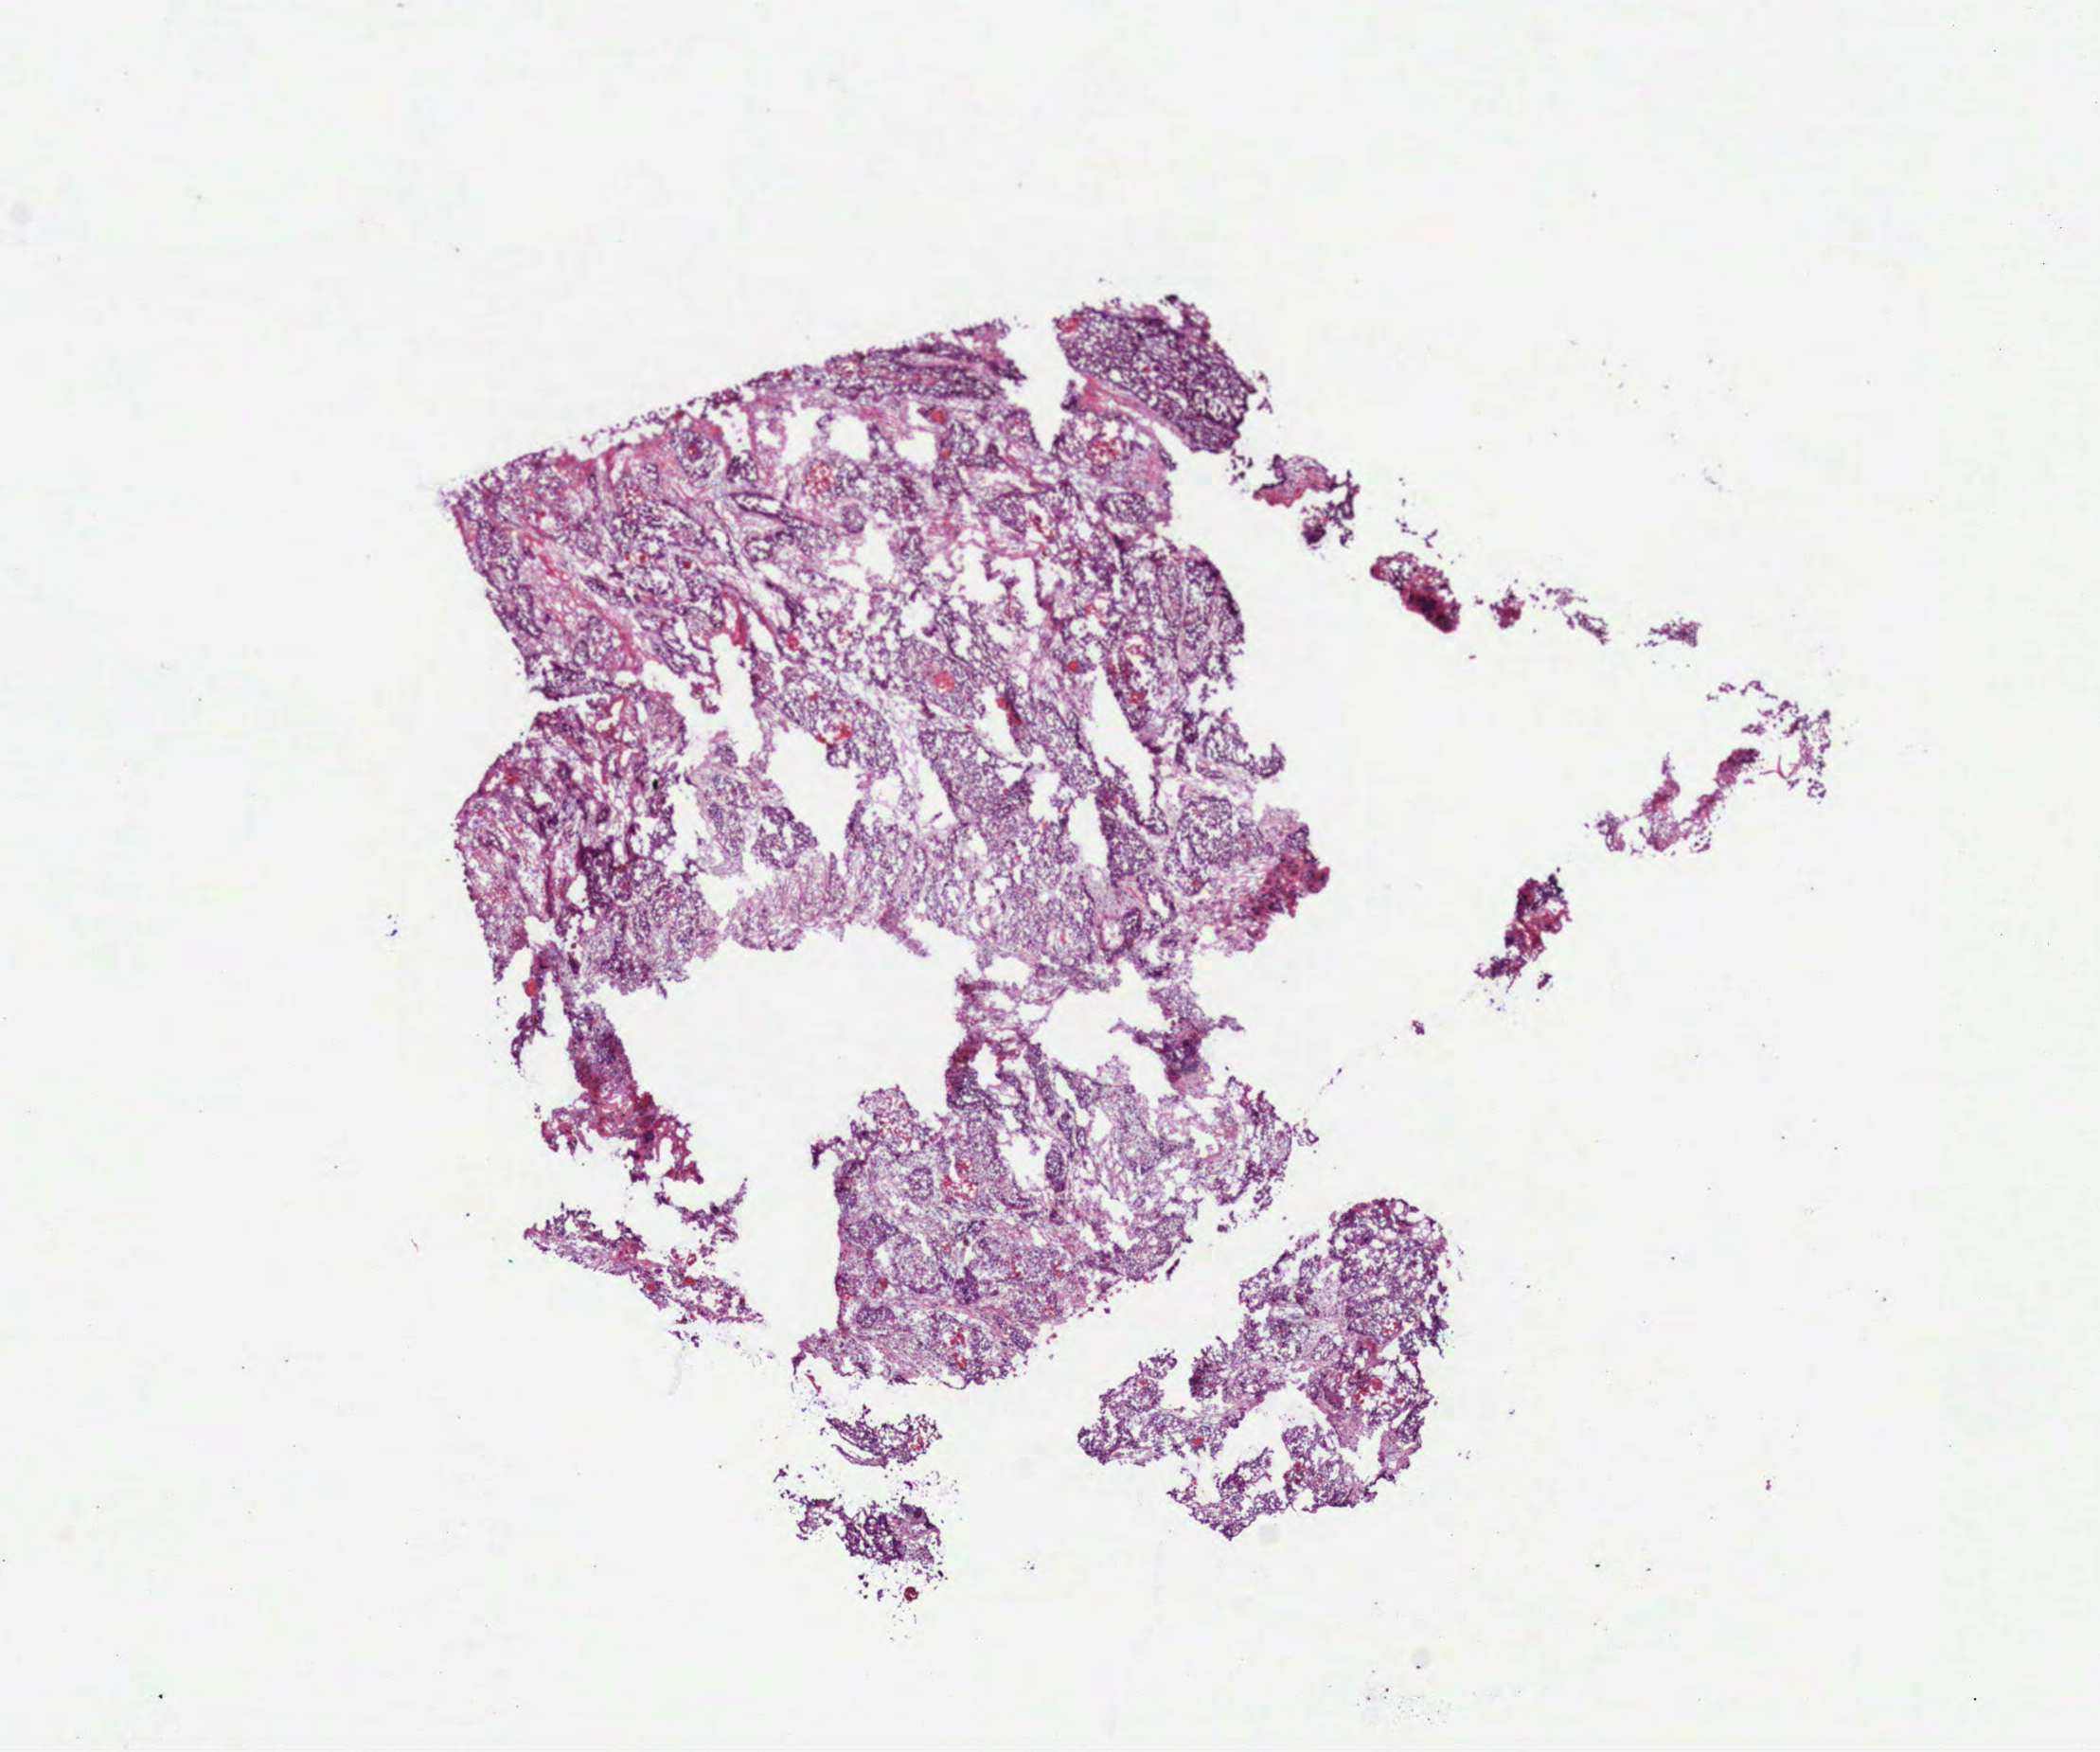
Digitized Hematoxylin and eosin (H&E) stained tissue section (whole slide), whole scanned area (about 8.9 x 7.5 mm) shown as a low-resolution overview. Frozen section. Primary tumour sample from the head and neck. Patient: female, age at initial diagnosis 80 years. Pathologist review of this section (percent, as recorded): tumour cells 95%, tumour nuclei 80%.
Pathologic diagnosis: Squamous cell carcinoma, NOS (cheek mucosa).